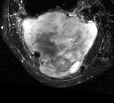
MRI of an extremity soft-tissue mass, one axial slice; position 24 of 44 along the scan axis; T2-weighted fat-saturated; MR volume resampled by the dataset authors to the PET/CT grid (not the native acquisition matrix); 114 × 103 image matrix, field of view 111 × 101 mm. Female patient. From the clinical record (not read from this slice): histological type: liposarcoma; site of the primary tumour: right thigh.
Annotated regions visible in this slice (expert contour drawn on MRI and transferred to this co-registered scan by the dataset authors):
- gross tumour volume (mass): bounding box (x1, y1, x2, y2) in pixels: (20, 11, 98, 78)